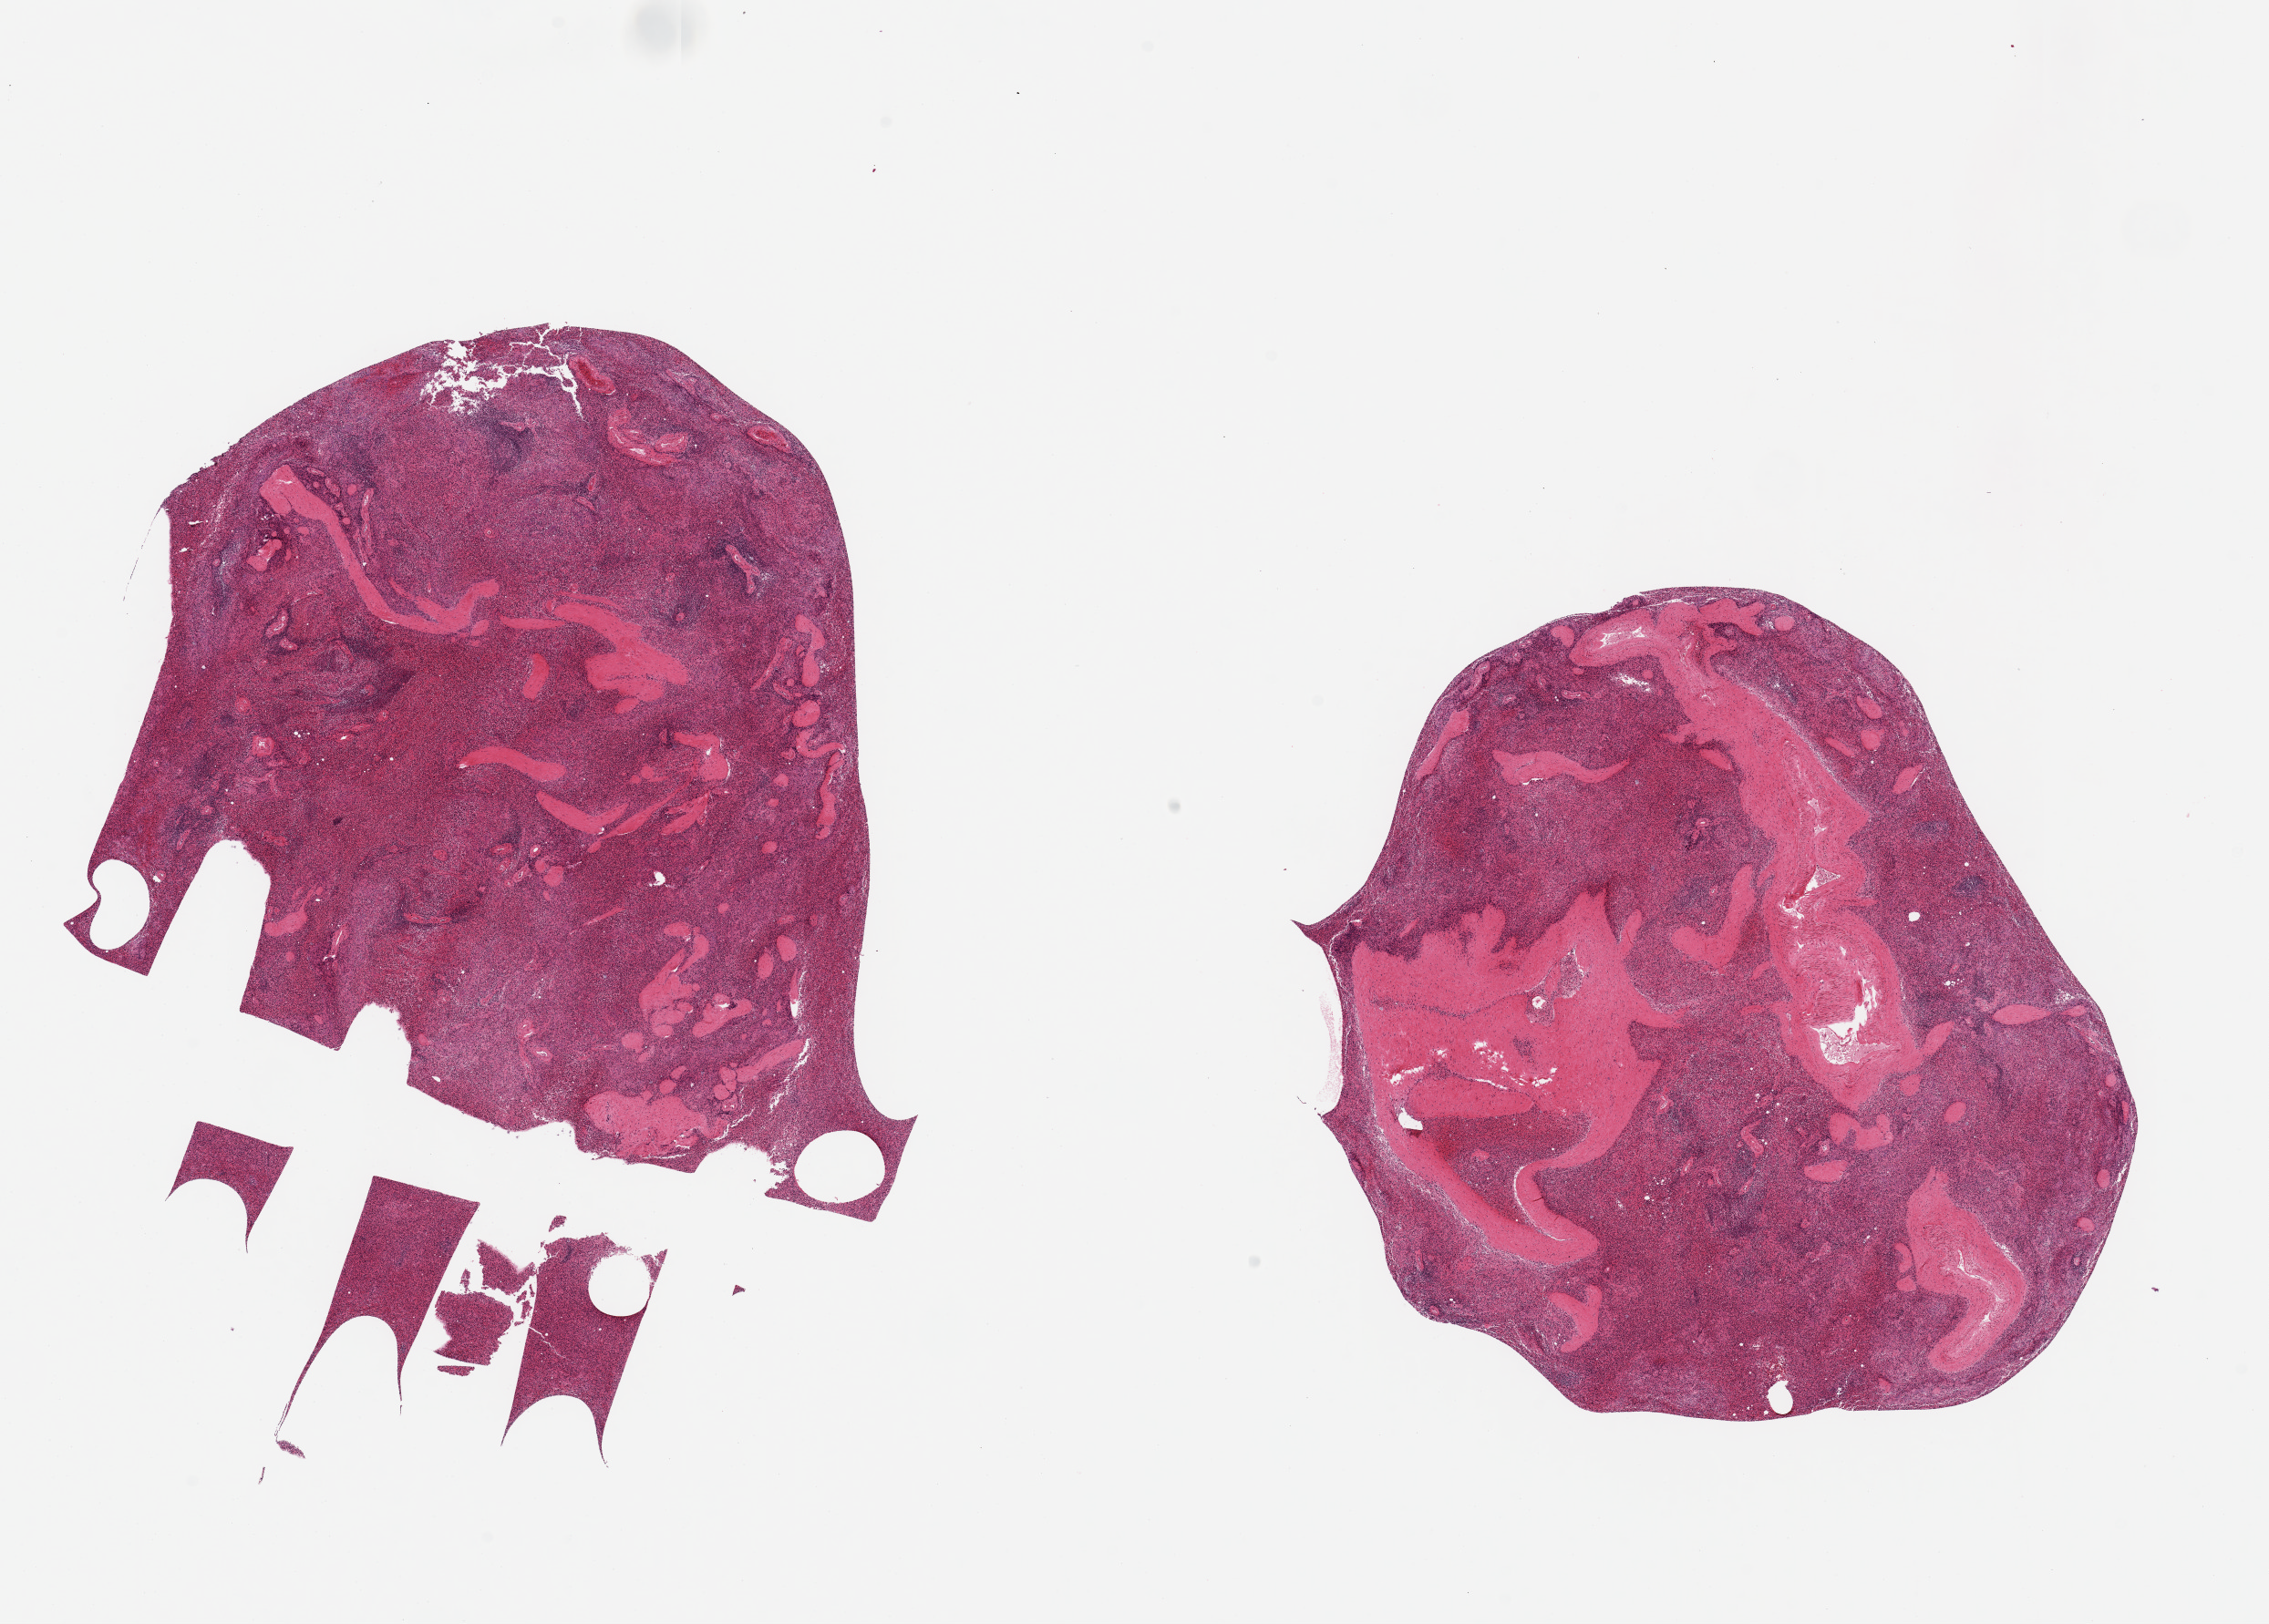
Whole-slide image, haematoxylin and eosin stain — whole scanned area (about 19.7 x 14.1 mm, slide scanned at 20x) shown as a low-resolution overview; PAXgene-fixed, paraffin-embedded tissue; sampled site (target tissue): spleen; donor tissue sample. Donor: male.
Review note (as recorded): 2 pieces, 10x8 & 7x7mm; congested.